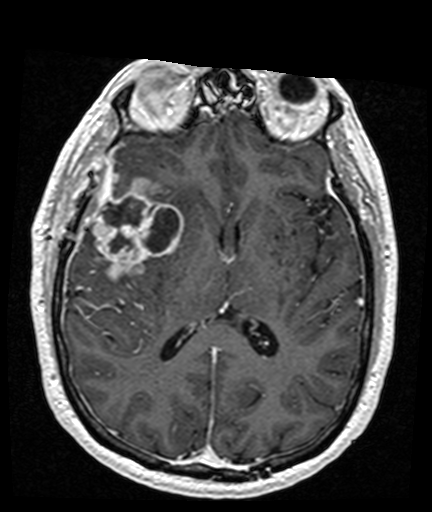
Brain MRI from a brain-tumour surgery series, one axial slice. Position 80 of 176 along the scan axis. T1-weighted post-contrast. 1 mm slice thickness. 432 × 512 image matrix, field of view 194 × 230 mm. From the clinical record (not read from this slice): histopathology: Glioblastoma; WHO grade: 4; IDH mutation: no.
Structures marked on this image (outlined manually by an expert reader):
- tumour: bounding box <93,176,183,281> (left, top, right, bottom; pixels)